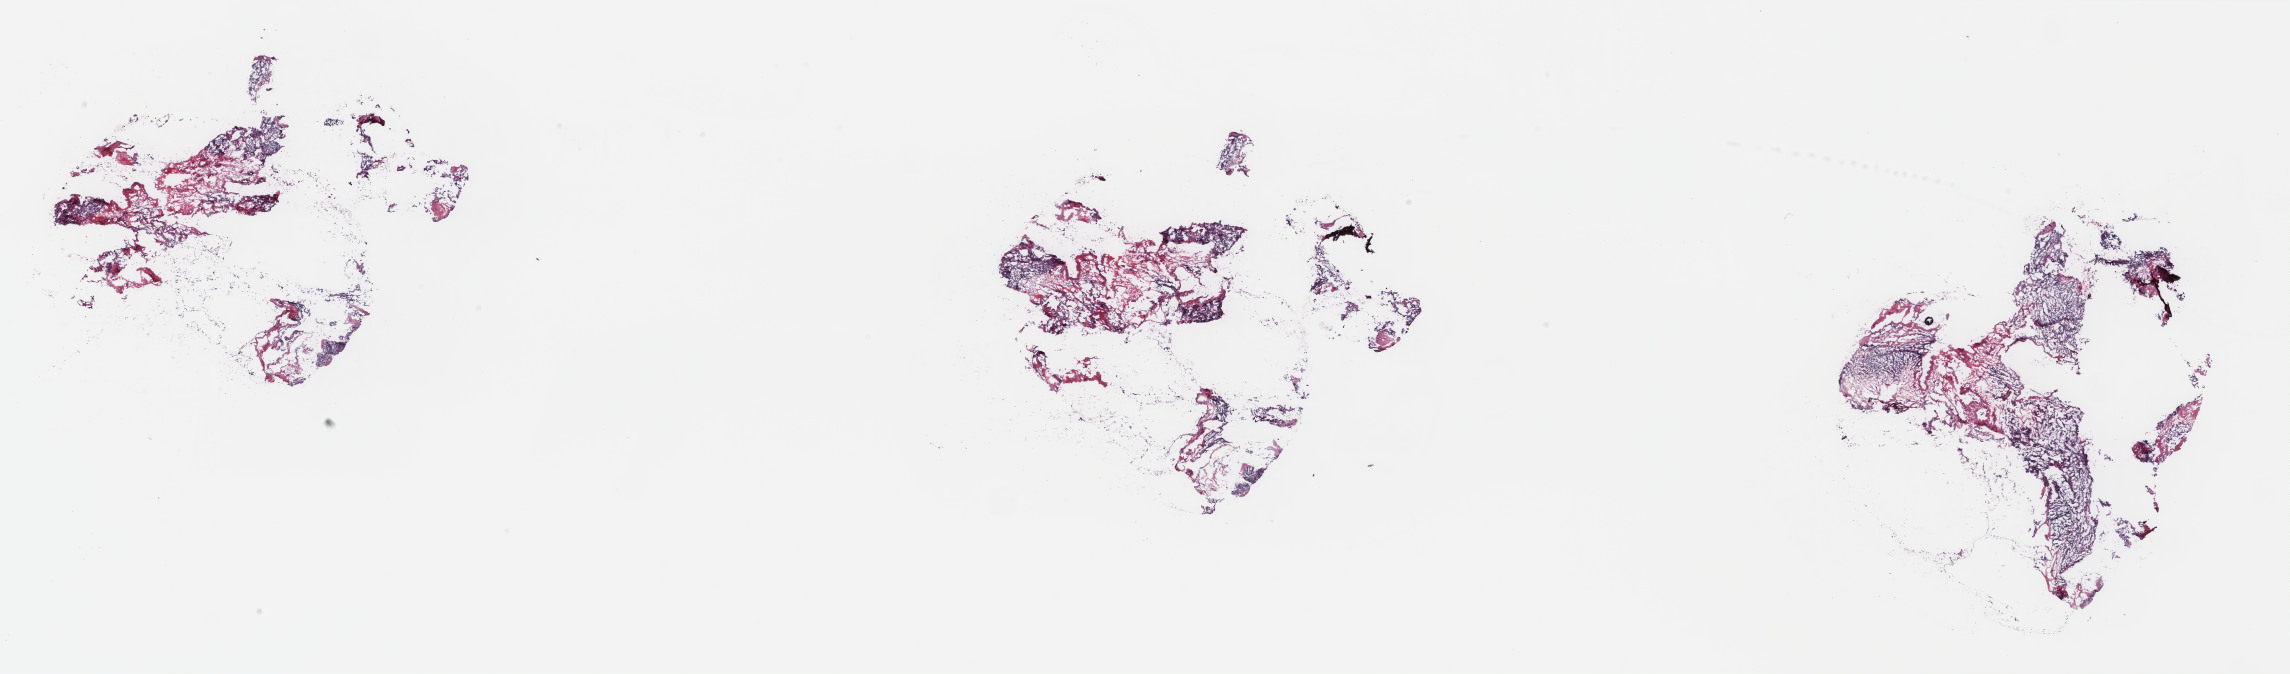
Whole-slide histology image, H&E, a low-resolution overview of the entire scanned area, about 36.4 x 10.7 mm (slide scanned at 40x). Frozen section from the top of the tissue portion. Thyroid, primary tumour sample. Male, age 28 years at initial diagnosis. Slide review estimates, as recorded: tumour cells 70%, tumour nuclei 70%, normal cells 0%, stromal cells 30%, necrosis 0%. Infiltration values recorded for this section: lymphocyte infiltration 10%, monocyte infiltration 0%, neutrophil infiltration 0%.
Lymph nodes positive (case pathology): 12 of 12 examined. TNM: TX N1b M0. Diagnosis: Papillary adenocarcinoma, NOS (thyroid gland). AJCC pathologic stage: I (5th edition).